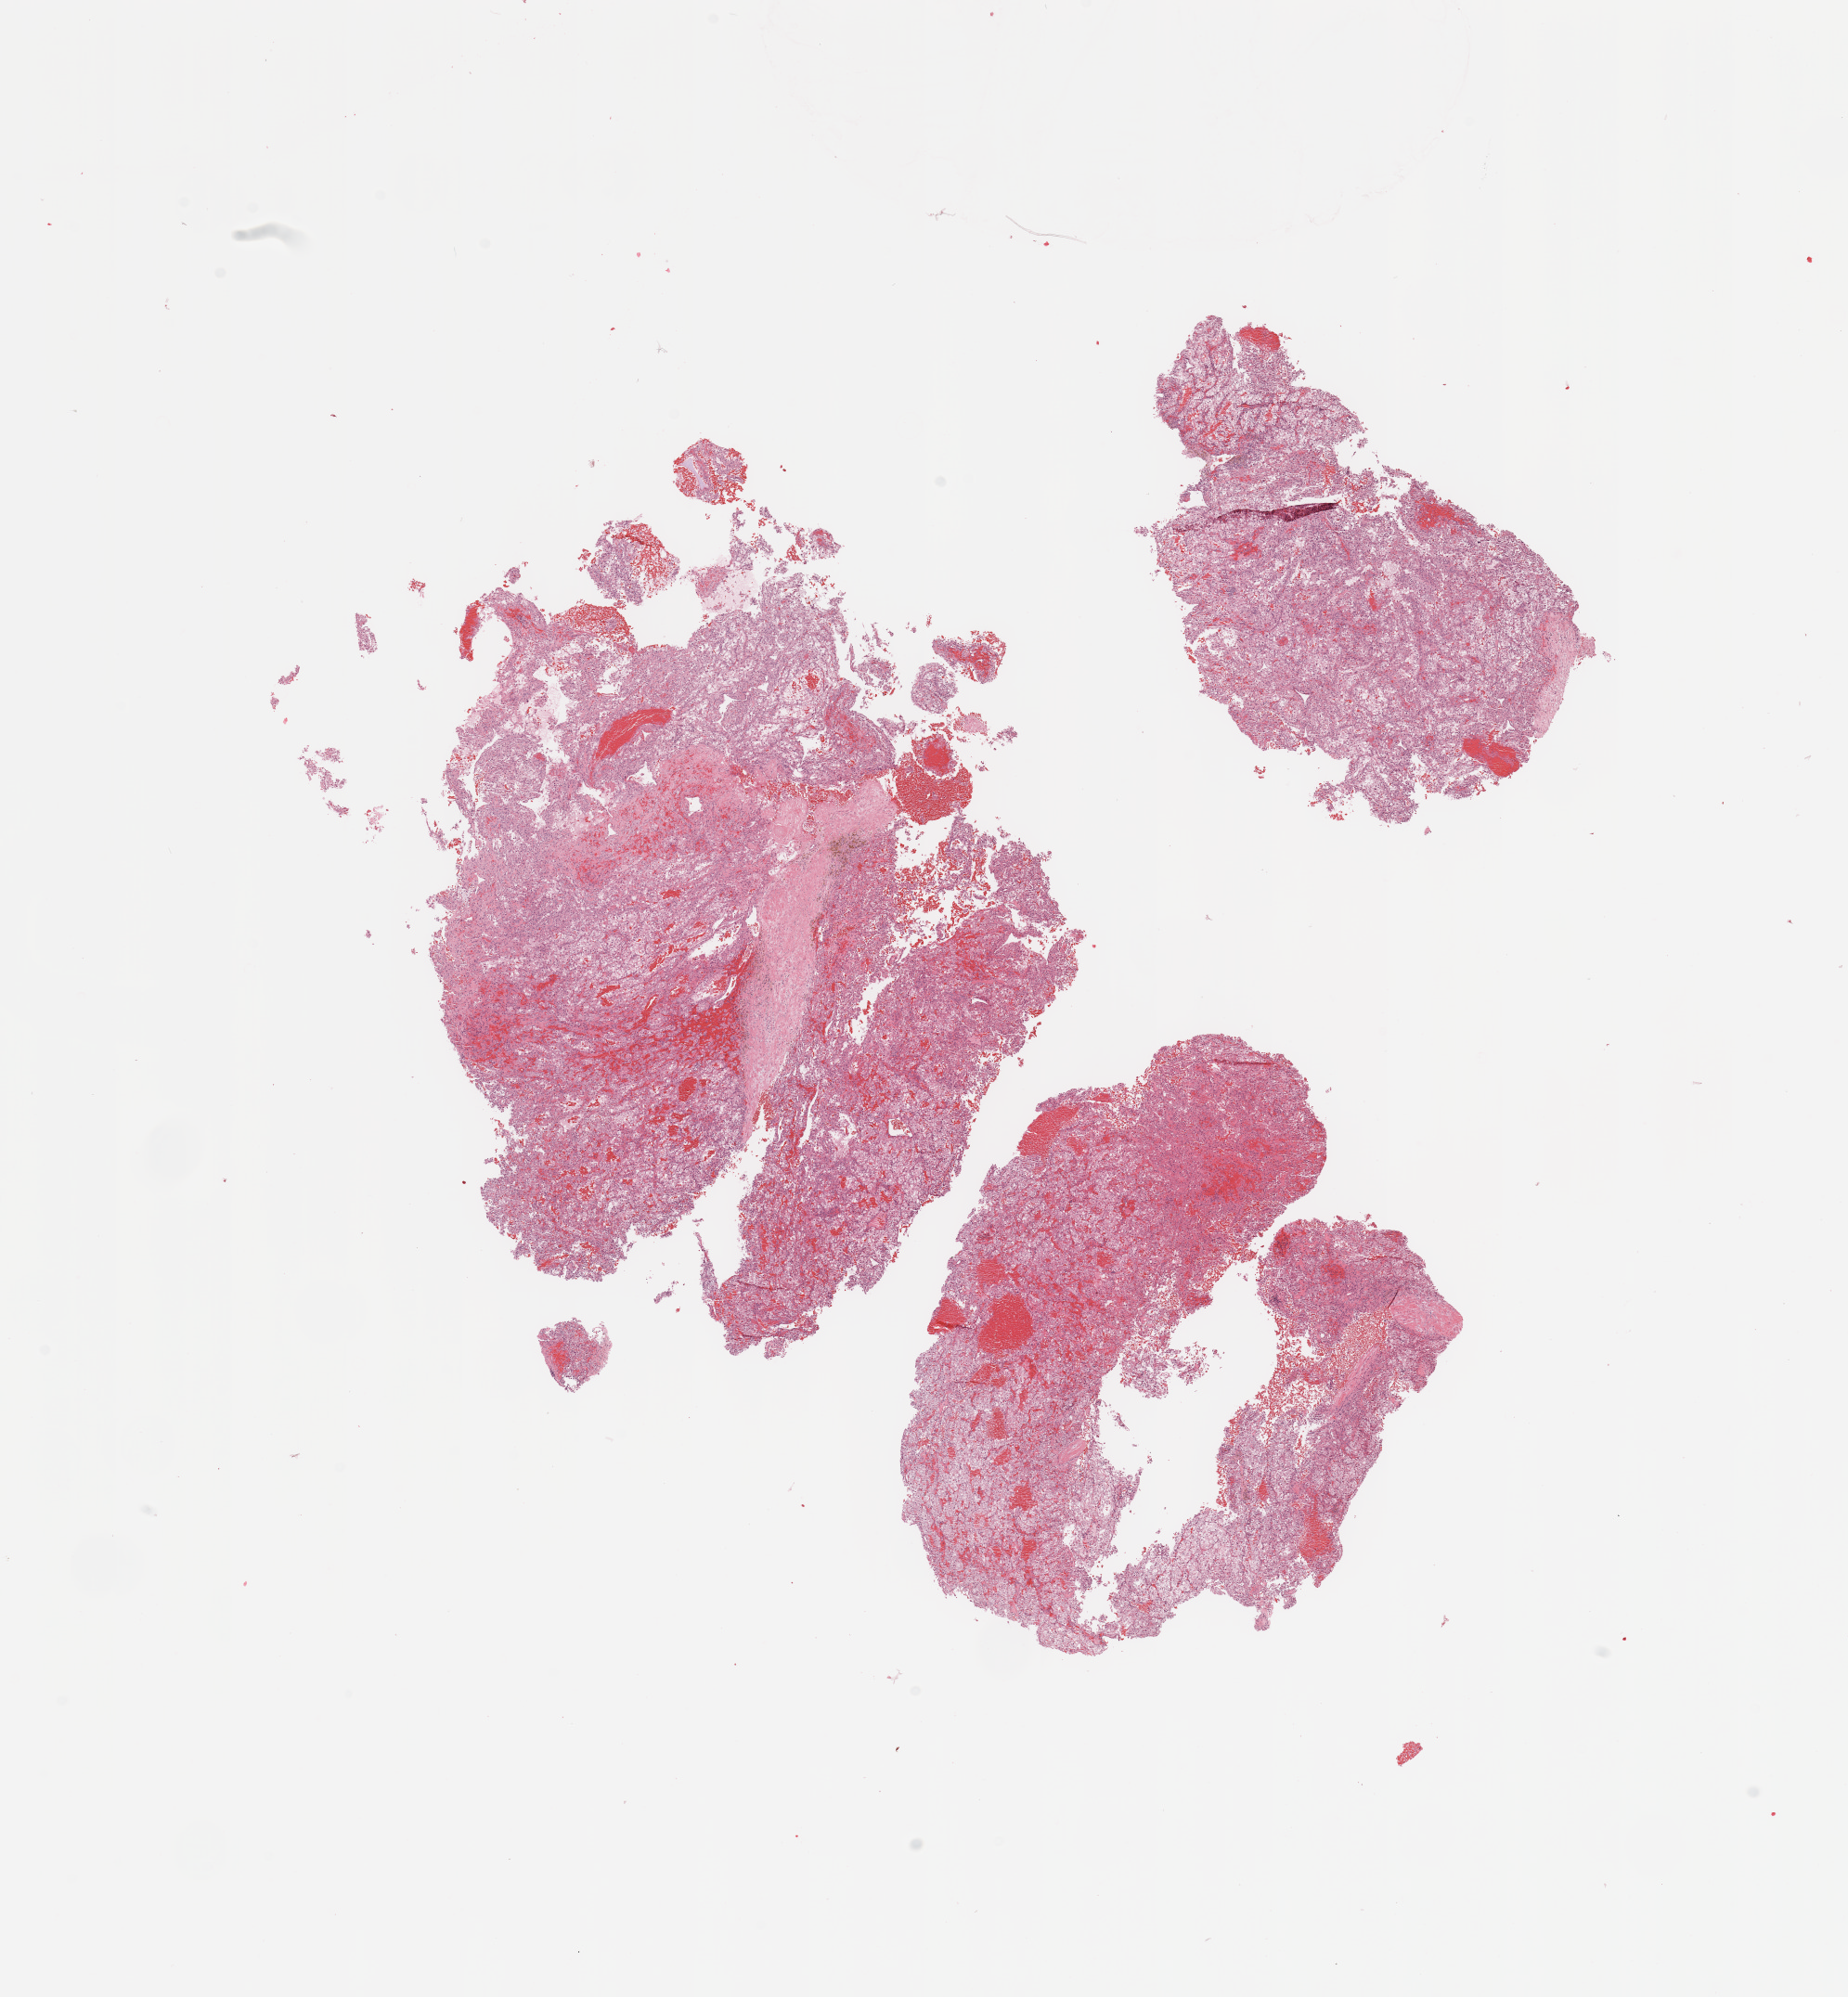
H&E-stained whole-slide image, a low-resolution overview of the entire scanned area, about 15.8 x 17.0 mm (slide scanned at 20x); tumour tissue sample, sampled site: kidney. Patient: female, age 89 years. Histologic grade: G2 (moderately differentiated). Slide review estimates, as recorded: tumour nuclei 80%, necrosis 5%.
• AJCC pathologic stage: III
• histologic diagnosis: Renal cell carcinoma, NOS